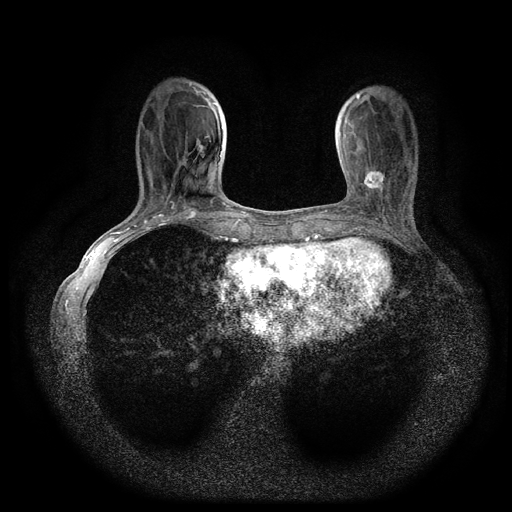
Breast MRI (dynamic contrast-enhanced, multi-phase), one axial slice; position 30 of 116 along the scan axis; dynamic contrast-enhanced series, time point 2 of 5 at this slice position (early post-contrast); 1.5 T; TE 2.7 ms, TR 5.4 ms; 2 mm slice thickness; 512 × 512 image matrix. Female patient, age 49 years.
Annotated regions visible in this slice (semi-automatic segmentation, software-assisted and operator-edited):
- breast lesion (labelled 'tumour' in the annotation; benign lesions carry a separate 'benign' label): bounding box [x1, y1, x2, y2] px = [361, 167, 385, 193]